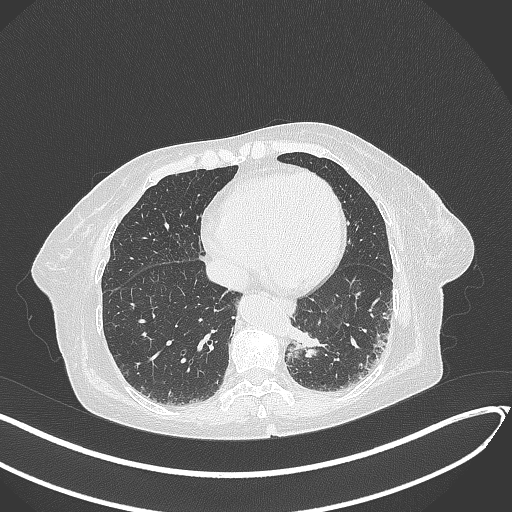
Chest CT, one axial slice. Position 64 of 324 along the scan axis. Reconstruction kernel B70f. Lung window (W 1500 / L -600 HU). 512 × 512 image matrix, field of view 400 × 400 mm. Female patient, age 82 years. Case-level facts recorded for this patient, not image findings: clinical TNM (as recorded): T1b N0 M1.
Annotated regions visible in this slice (bounding box drawn by a radiologist):
- lung tumour (recorded histology: adenocarcinoma): bounding box (x1, y1, x2, y2) in pixels: (290, 325, 324, 361)